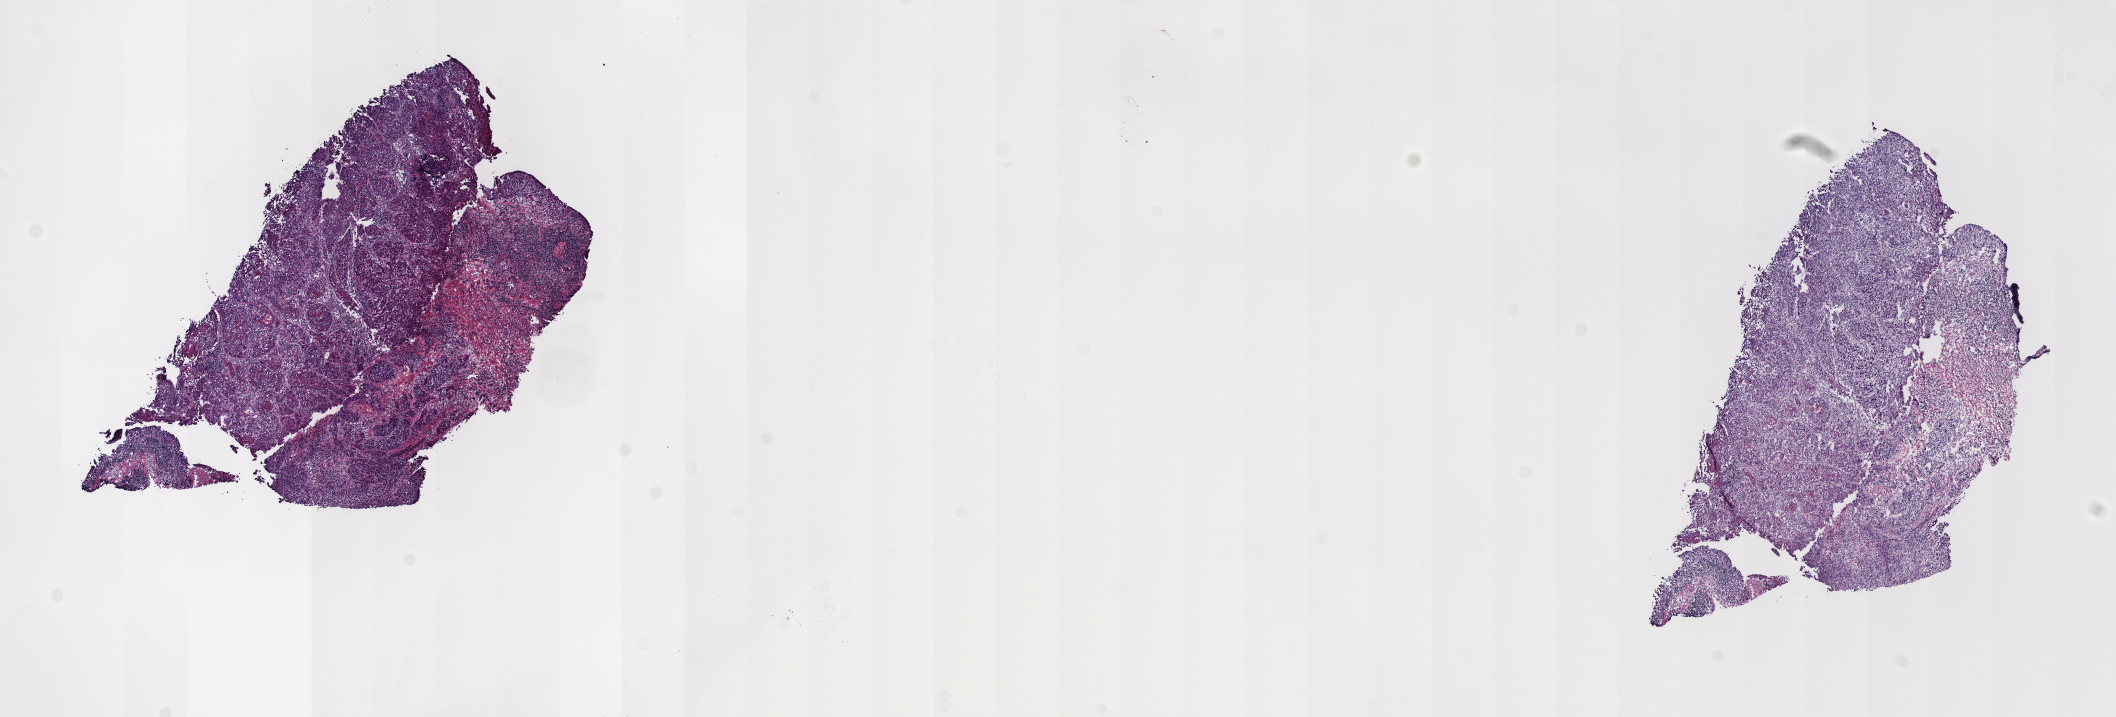
Digitized H&E tissue section (whole slide) — whole scanned area (about 17.1 x 5.8 mm, from a 40x scan) shown as a low-resolution overview; frozen section; sample: primary tumour, cervix. Patient: female, age at initial diagnosis 39 years. Pathologist review of this section (percent, as recorded): tumour cells 80%, tumour nuclei 80%, normal cells 5%, stromal cells 15%, necrosis 0%. Inflammatory infiltration, as recorded: lymphocyte infiltration 10%, monocyte infiltration 0%, neutrophil infiltration 0%.
FIGO stage: IB1. Histologic diagnosis: Squamous cell carcinoma, NOS (cervix uteri). Lymph nodes positive (case pathology): 0 of 33 examined.